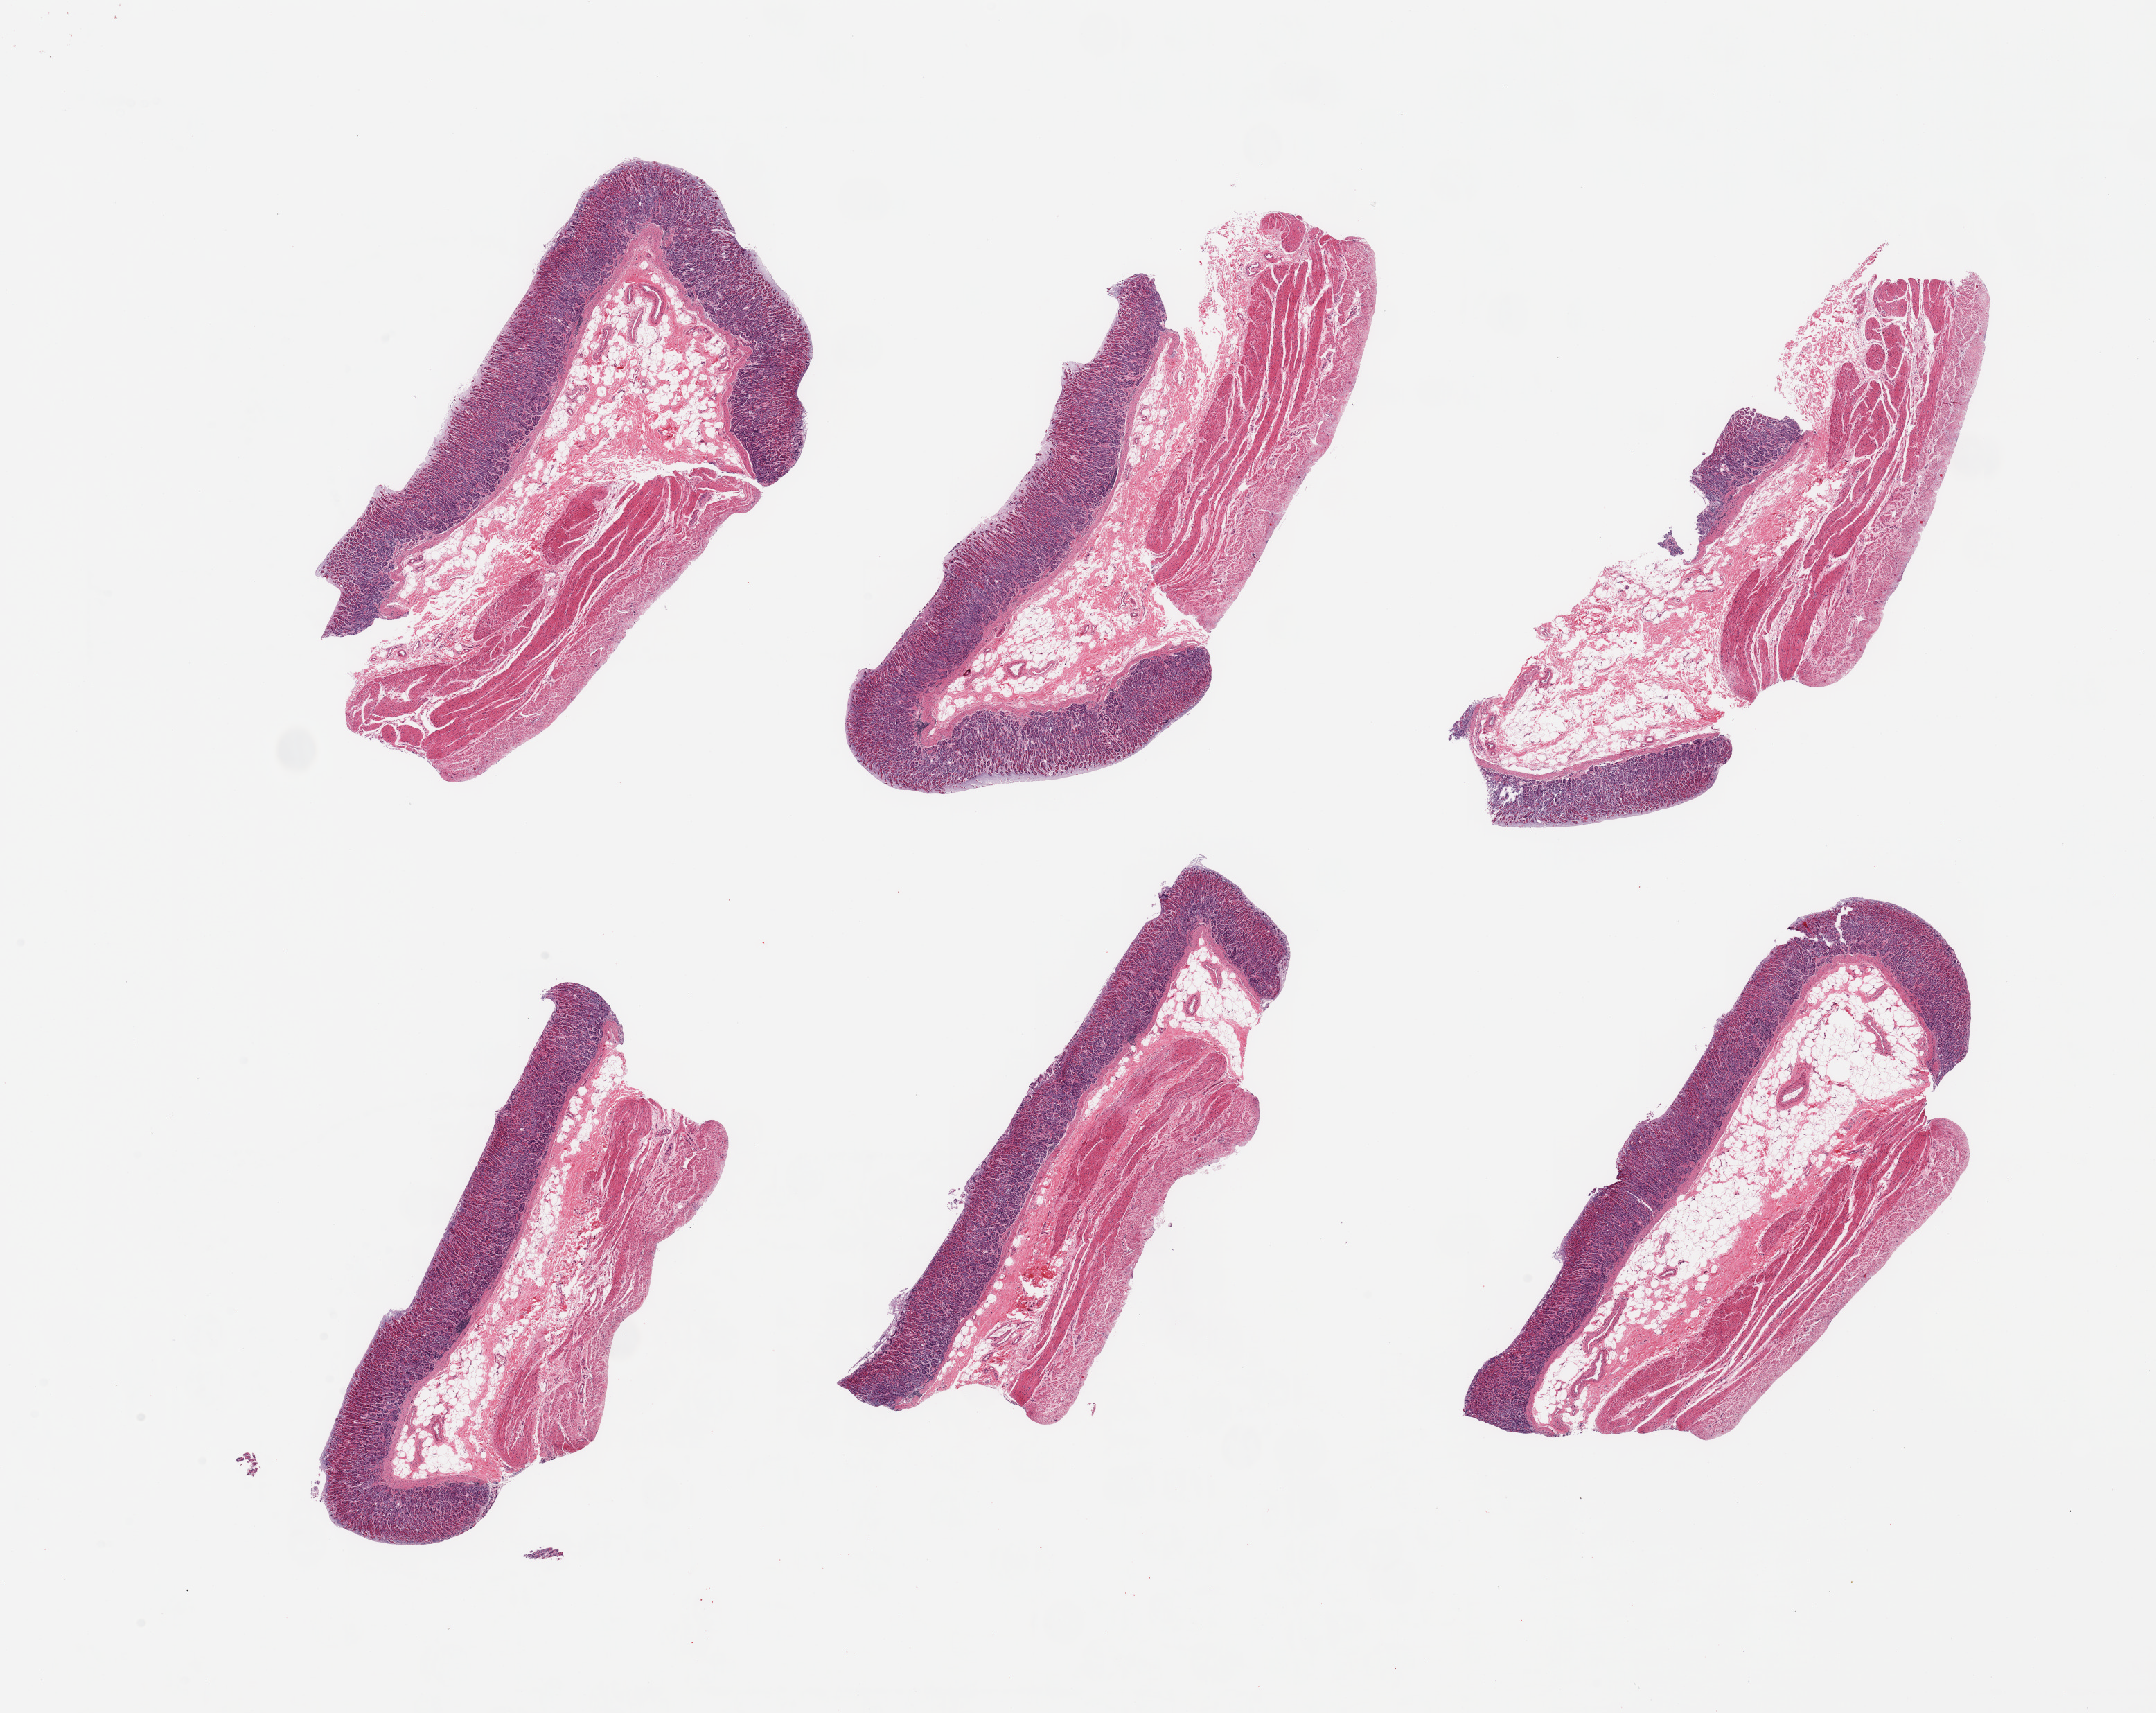
Whole-slide image, H&E stain — shown as a low-resolution overview of the whole scanned area (about 24.6 x 19.5 mm). PAXgene-fixed paraffin-embedded (PFPE) section. Section of stomach (target tissue). Tissue donor sample. Donor sex: male.
Reviewer comment on this tissue sample: 6 pieces, mucosa 0.6-1.0mm, 30-40% of thickness. Some foci approach score 2 near luminal surface.